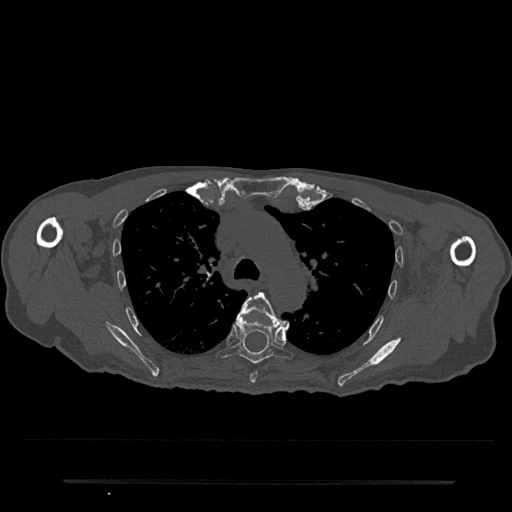
CT including the spine, one axial slice. Slice 545 of 797 in the series (ordered by position). 120 kVp. Bone window (W 1800 / L 400 HU). 0.5 mm slice thickness. 512 × 512 image matrix. Patient: male, 74 years. Case-level facts recorded for this patient, not image findings: primary cancer: prostate.
Structures marked on this image (semi-automatic segmentation, software-assisted and operator-edited):
- T5 vertebra: bounding box <239,292,289,383> (left, top, right, bottom; pixels)
- T6 vertebra: <216,314,293,364>